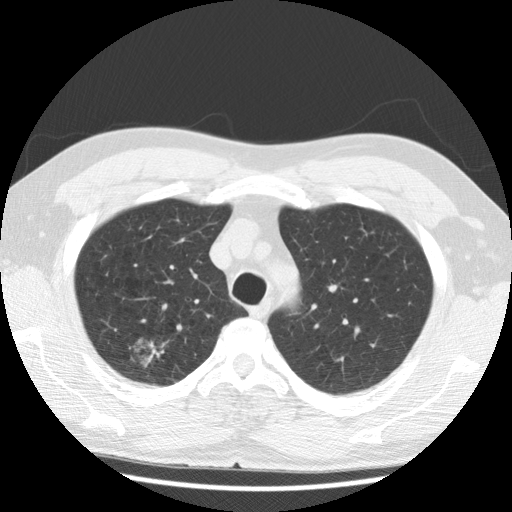
Low-dose screening chest CT, axial slice; first (baseline) screen; lung window (W 1500 / L -600 HU); 2.5 mm slice thickness; 512 × 512 image matrix. Male, age 59 years at enrolment. Former smoker at enrolment.
Expert reader's lesion annotation, box from (x=107, y=322) to (x=178, y=390) px. The exam's reader record, not a measurement of the box and not confirmed to be the same lesion: non-calcified nodule or mass ≥4 mm, right upper lobe, 30 × 28 mm, poorly defined margins, ground glass attenuation. Participant outcome: lung cancer diagnosed 40 days after this screen — bronchiolo-alveolar carcinoma, non-mucinous, right upper lobe, well differentiated (G1), stage IA (AJCC 6th edition), 15 mm at pathology.